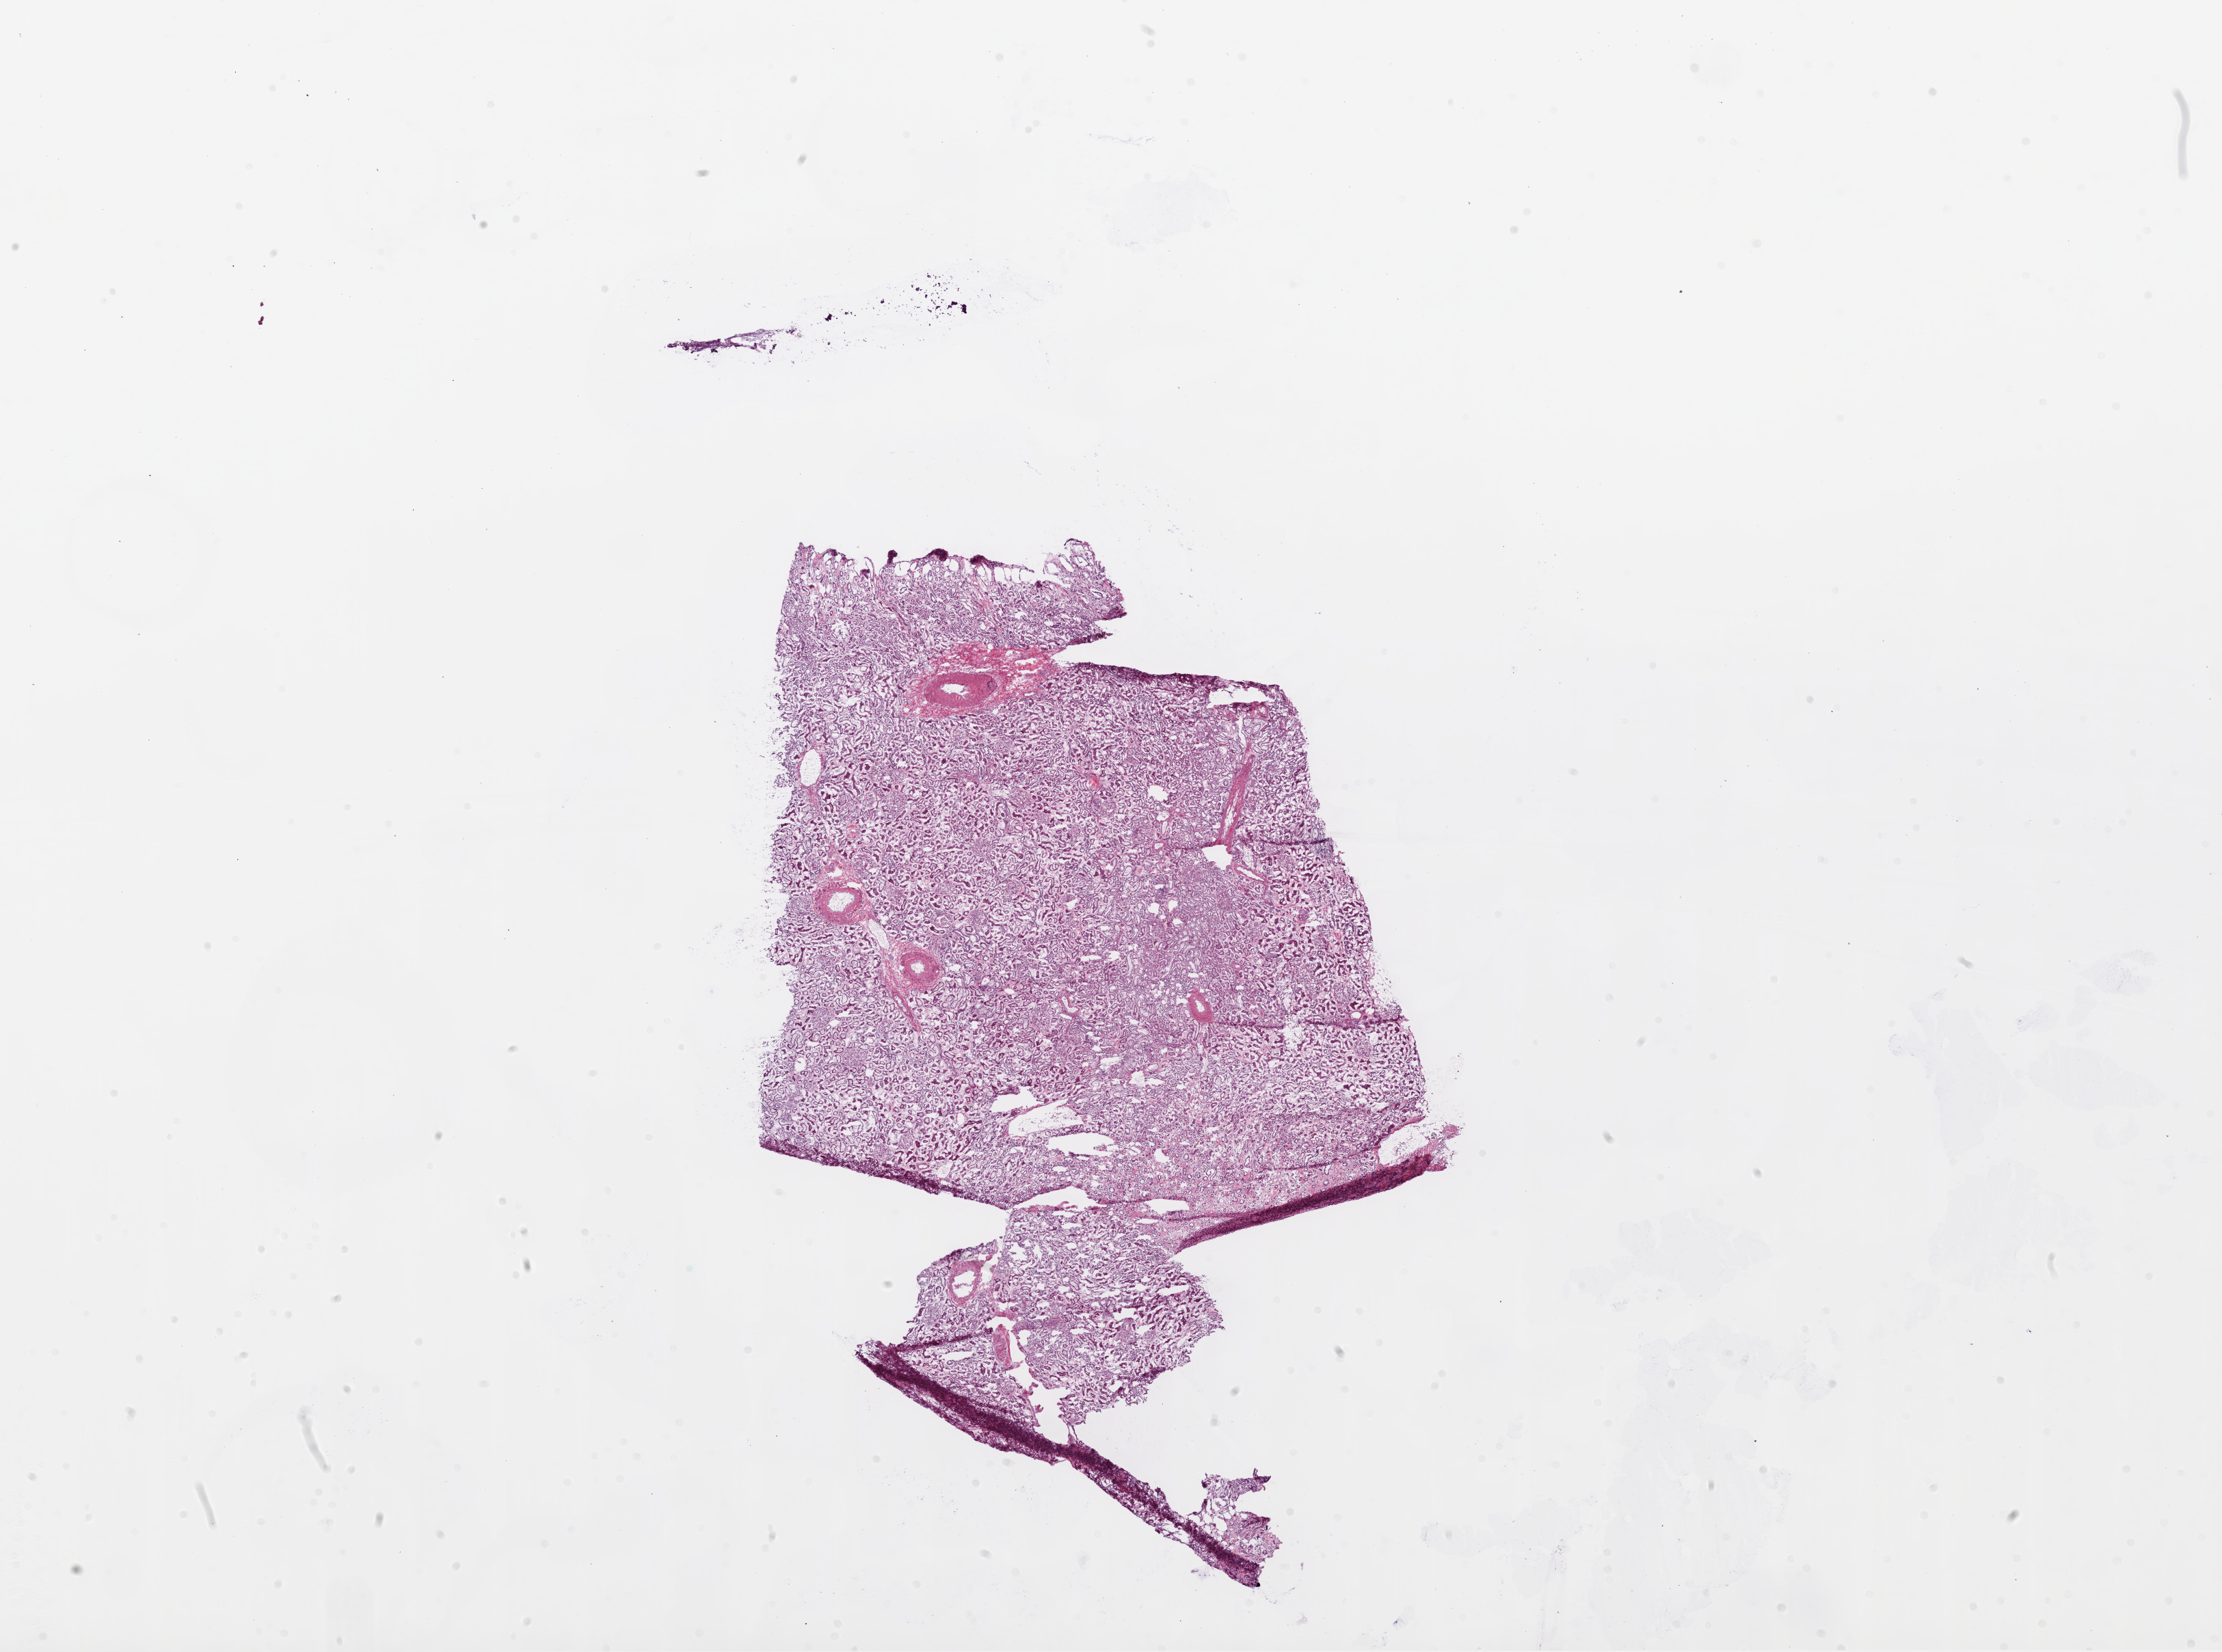
Whole-slide histology image, H&E, low-resolution overview of the scanned area, about 26.1 x 19.4 mm; frozen section from the top of the tissue portion; sample: solid tissue normal (non-tumour tissue), kidney. Patient: female, age at initial diagnosis 57 years.
This section: solid tissue normal sample (biorepository sample class). Patient diagnosis: Clear cell adenocarcinoma, NOS.